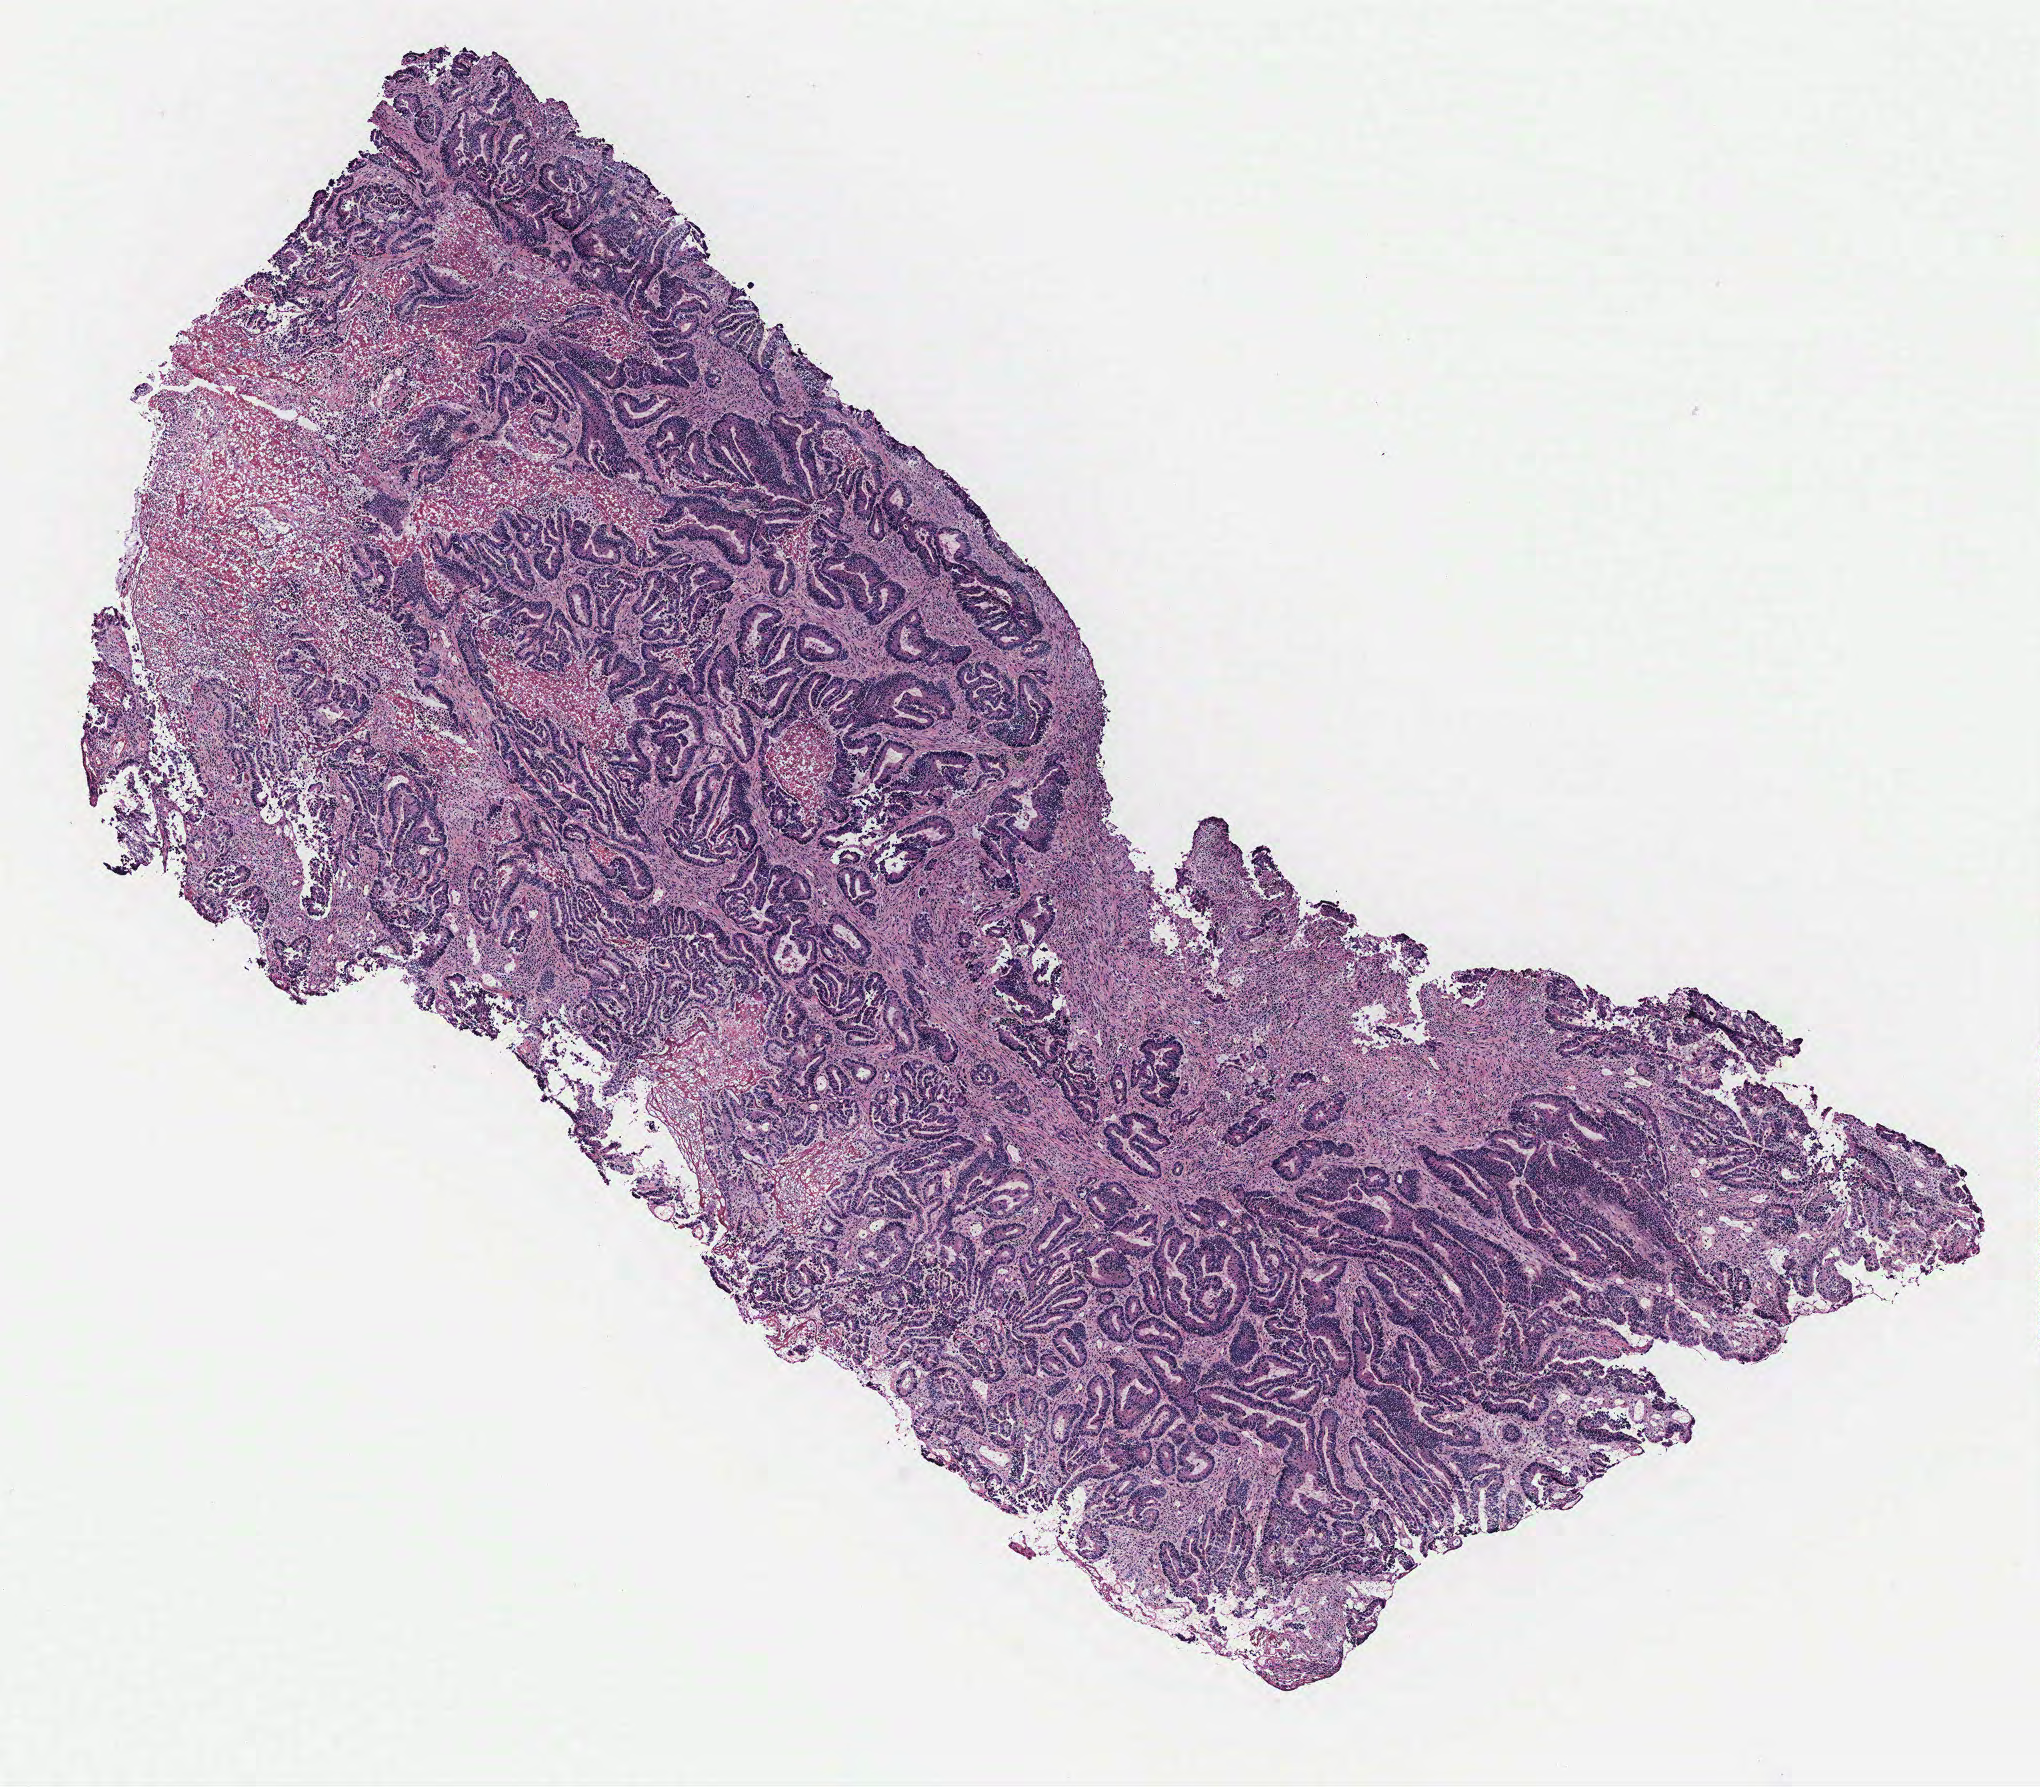
H&E-stained whole-slide image, whole scanned area (about 8.2 x 7.2 mm) shown as a low-resolution overview, colon, tissue type not recorded.
• patient diagnosis (cohort enrolment): colon cancer (colon)